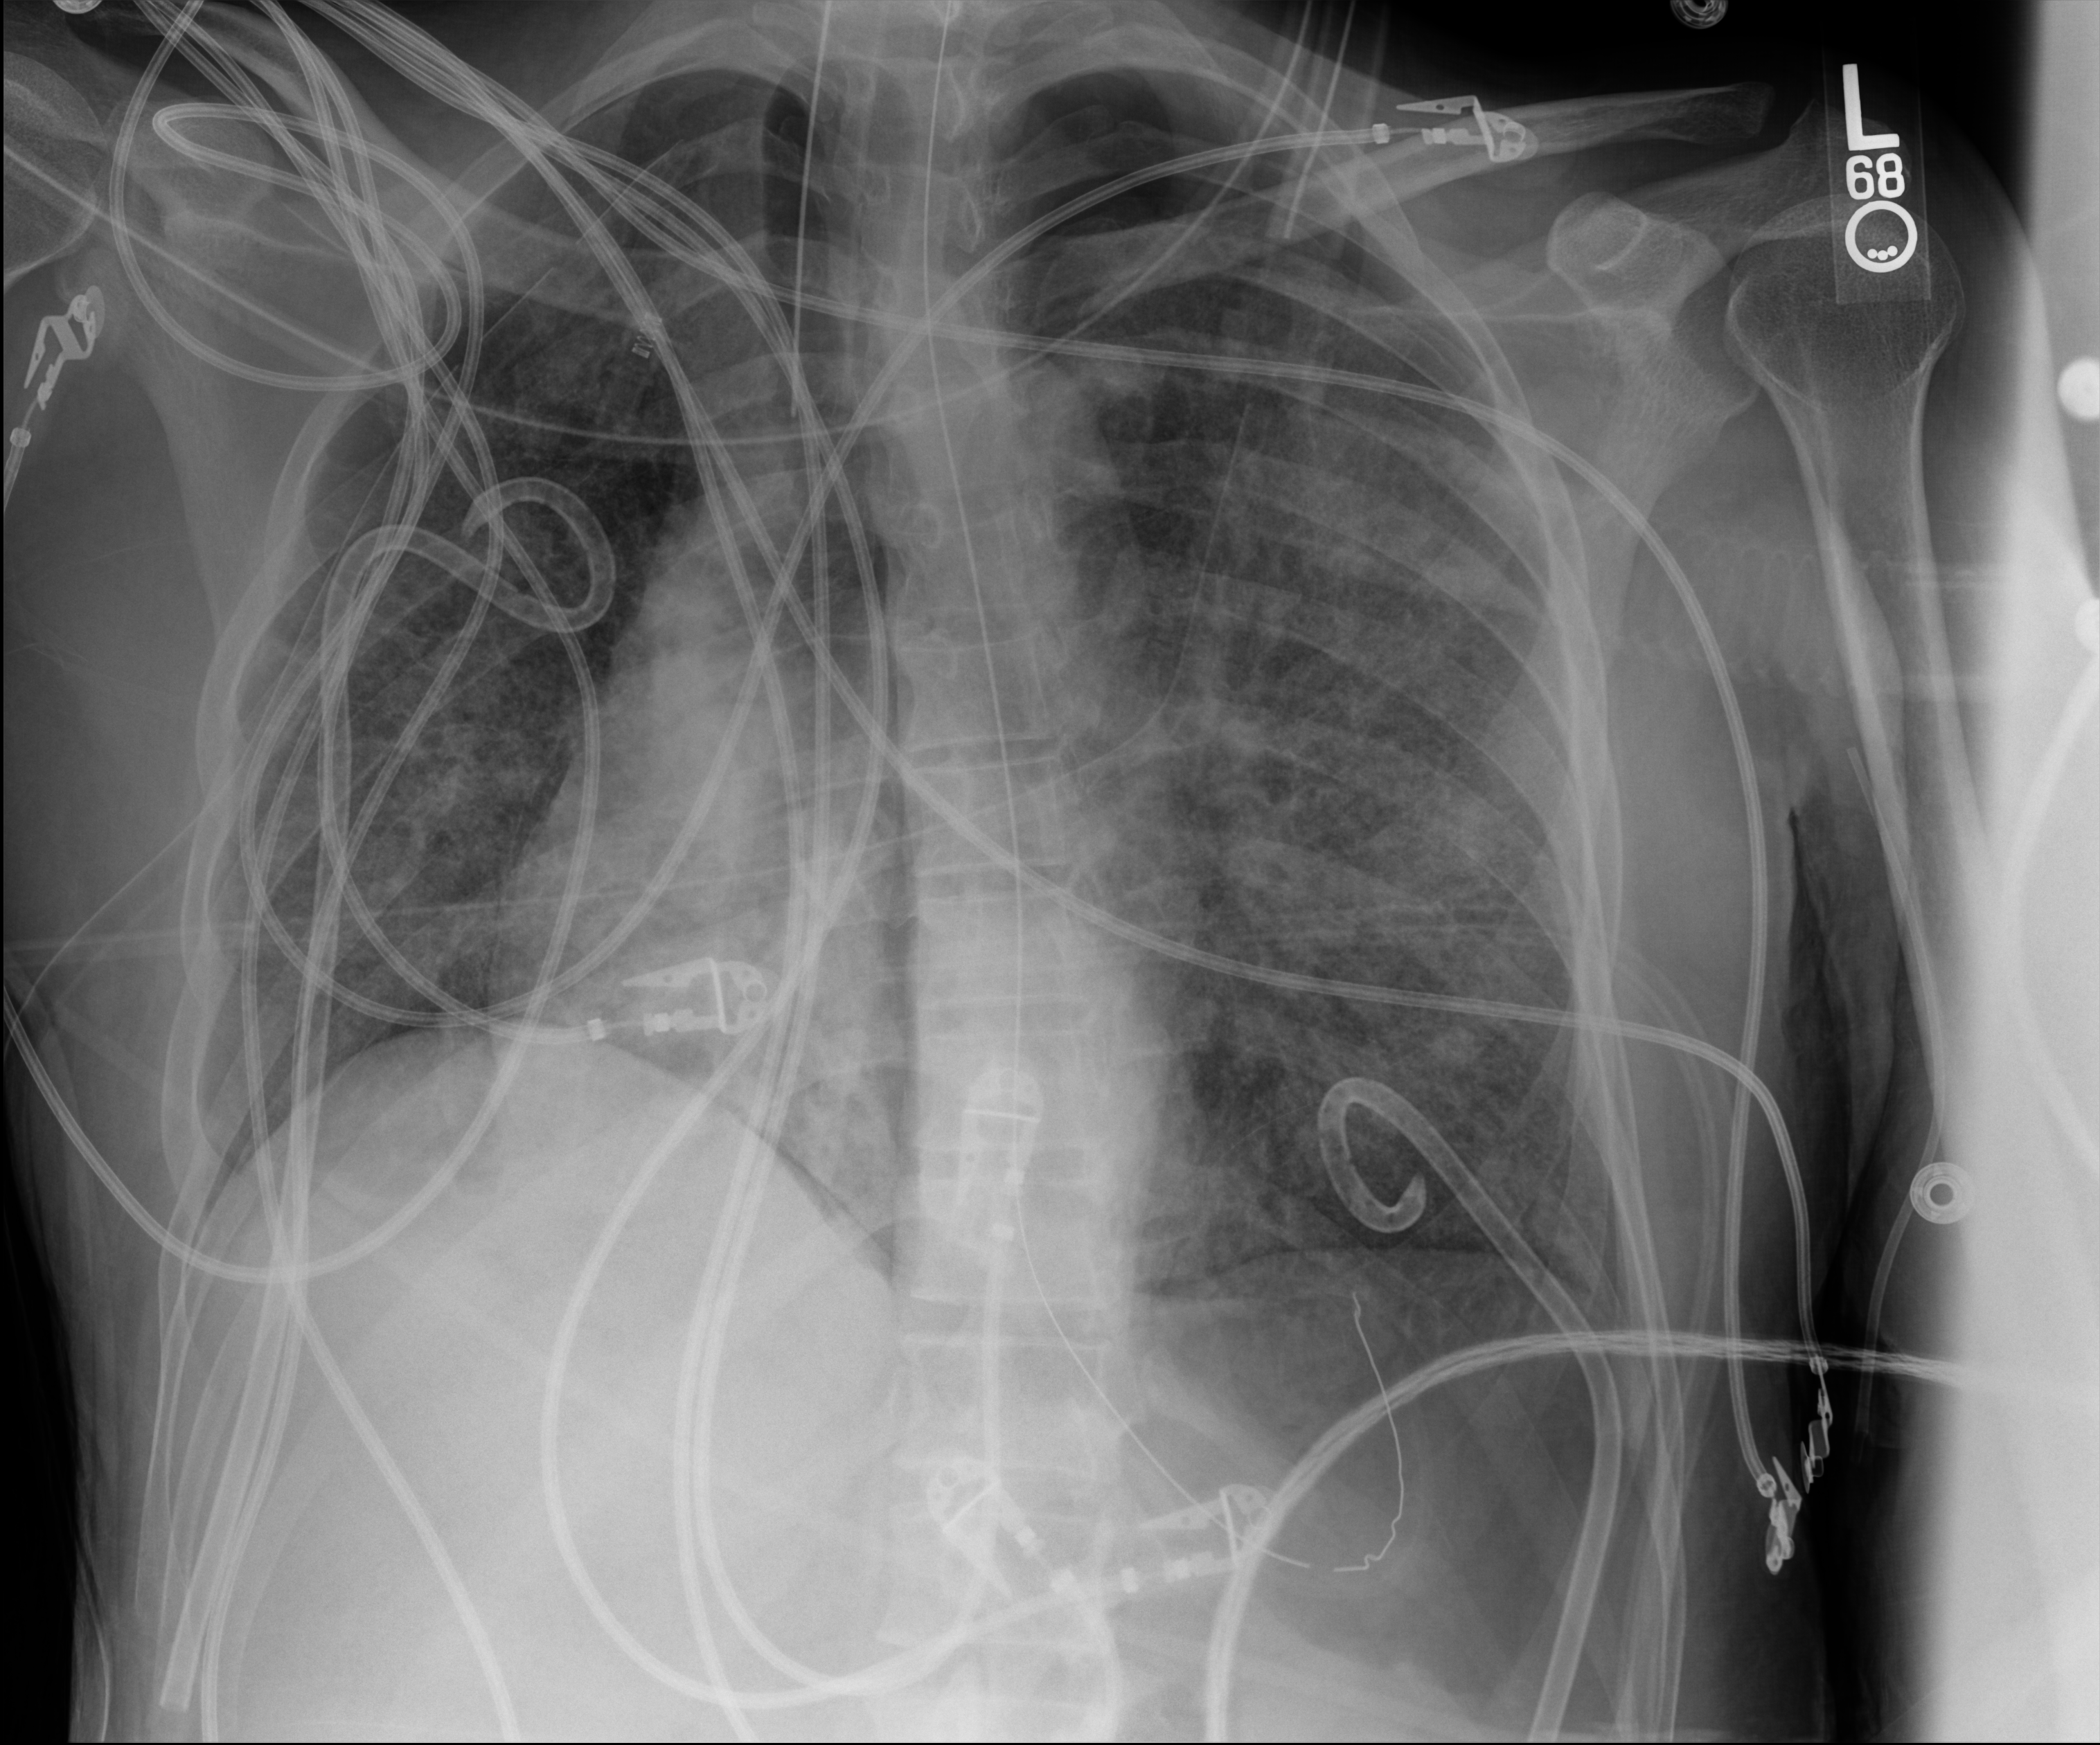
Chest X-ray (portable), anteroposterior (AP) projection. Patient hospitalised with COVID-19, aged 18–59 years.
Hospital-stay facts (about this admission, not read from this image; timing relative to this image not recorded): admitted to intensive care during this hospital stay: yes.